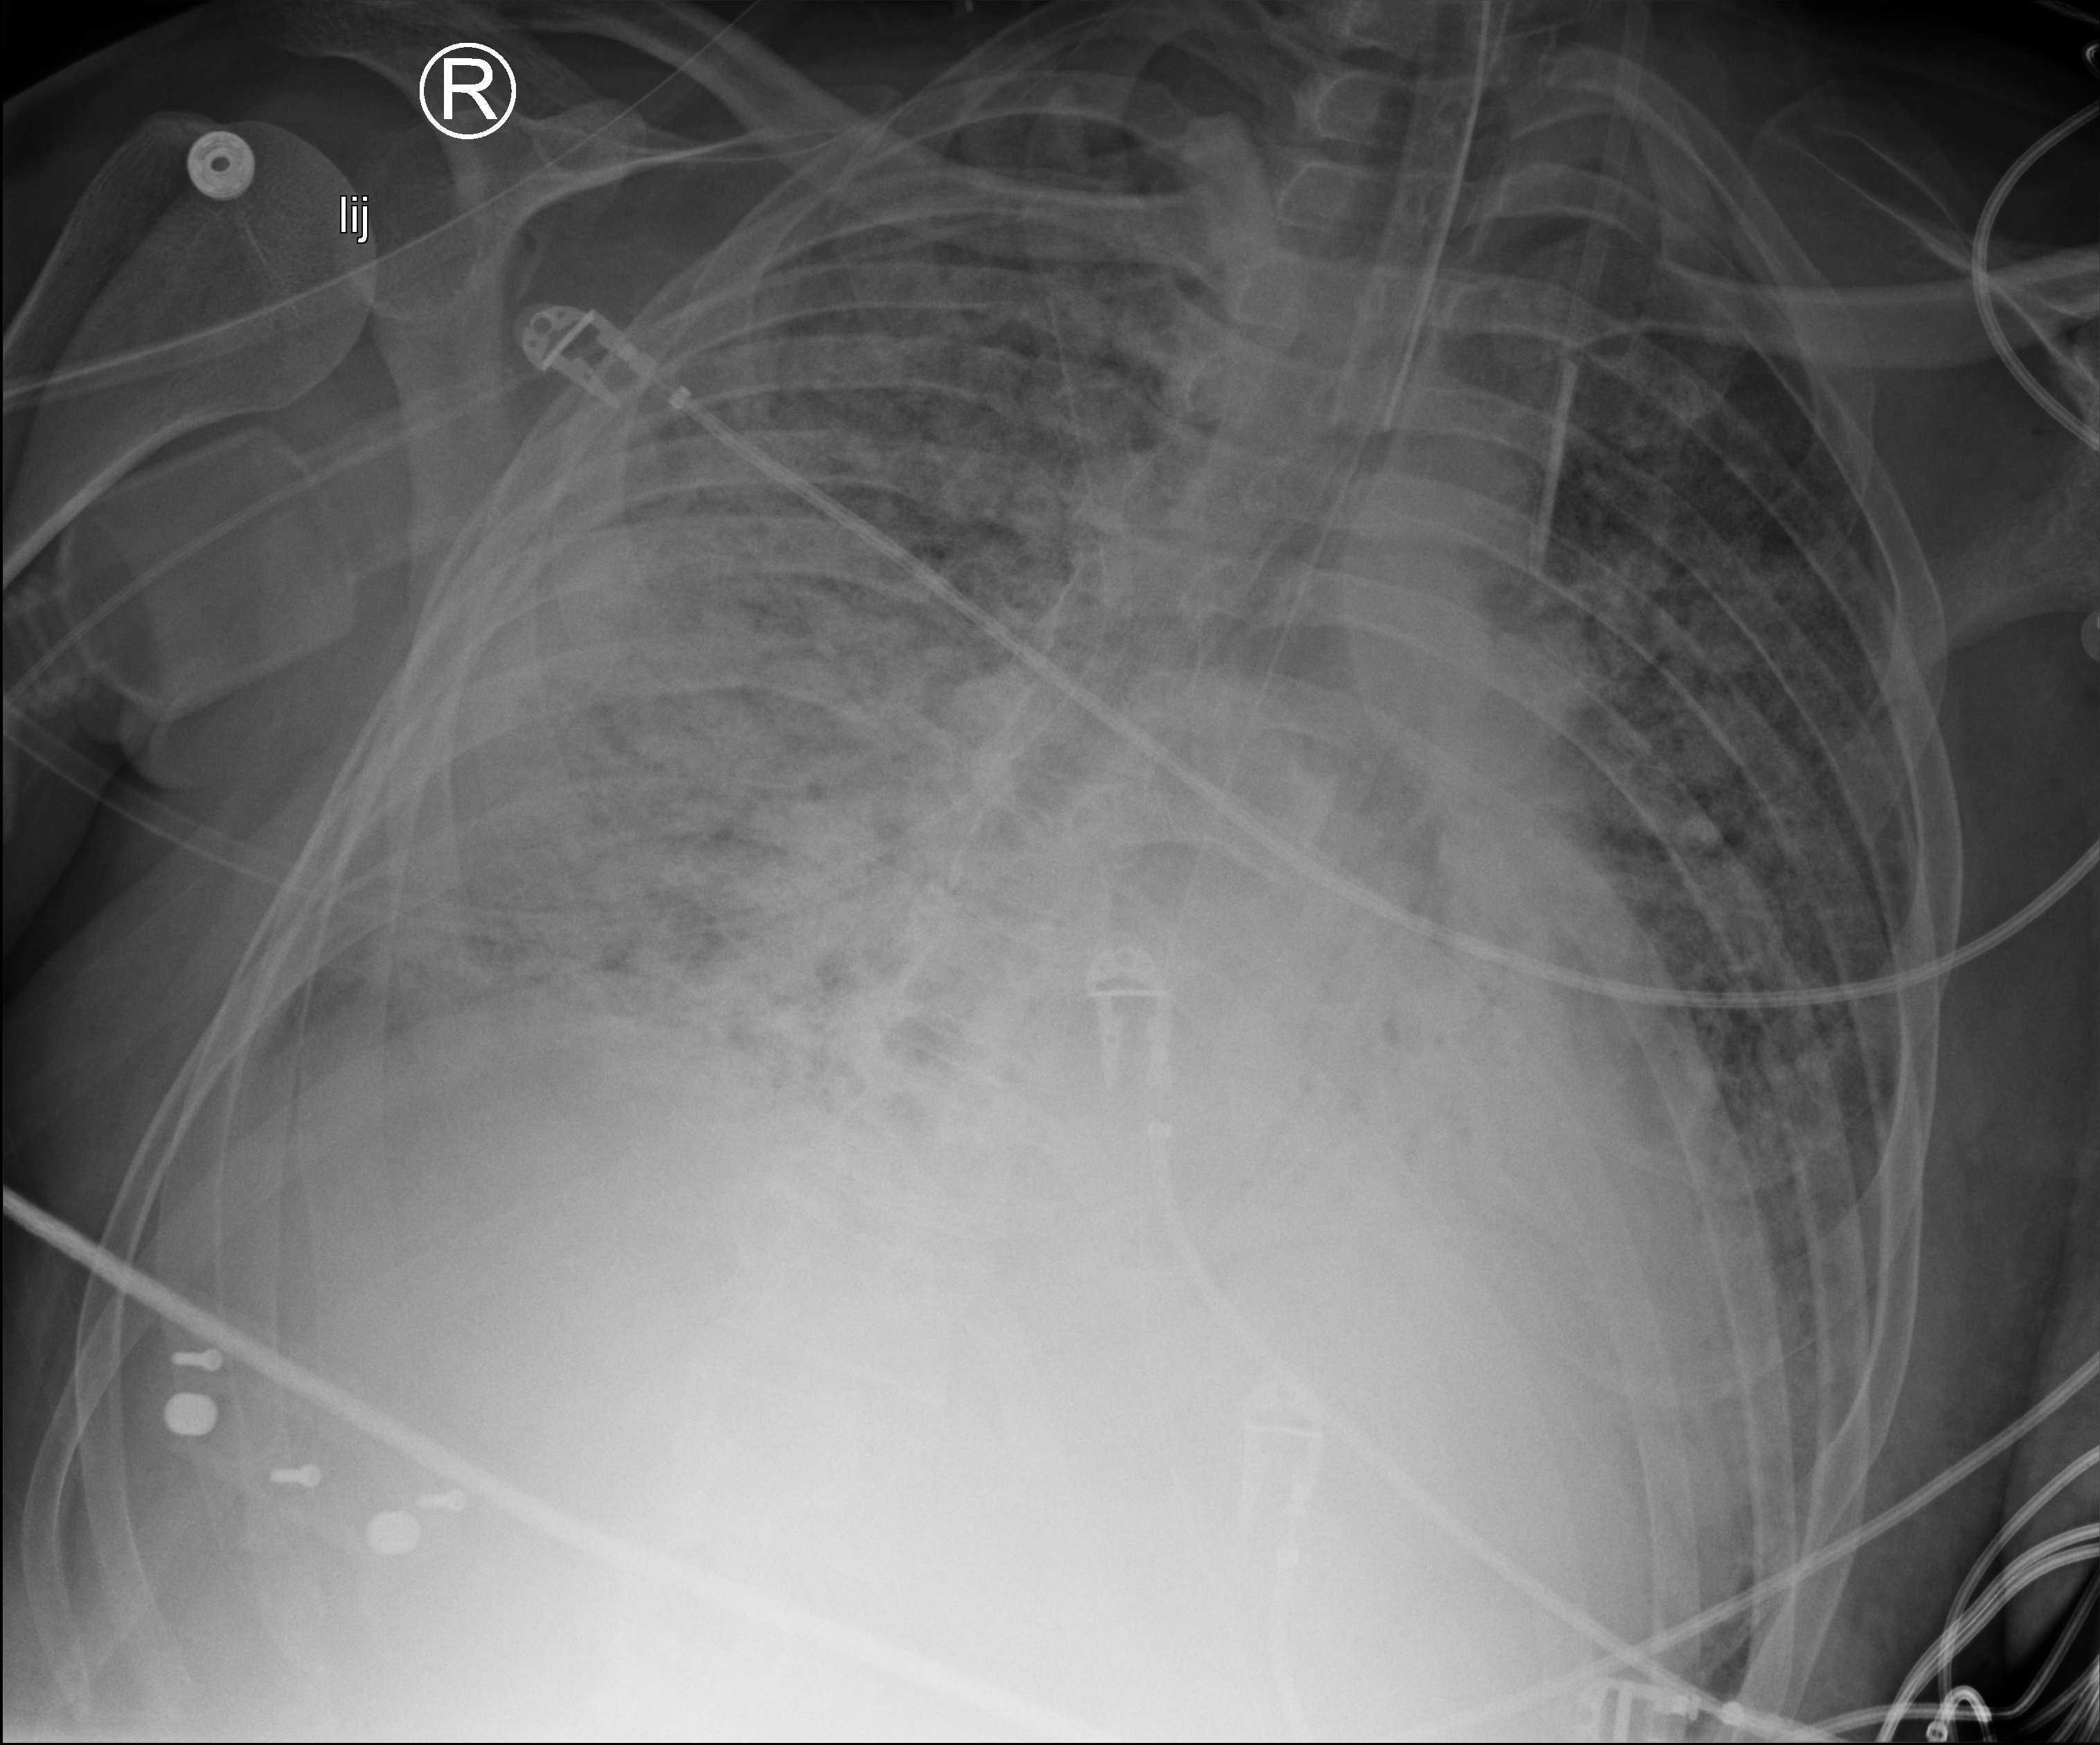
Bedside chest radiograph (computed radiography), anteroposterior (AP) projection. Patient hospitalised with COVID-19; male, aged 18–59 years.
Hospital-stay facts (about this admission, not read from this image; timing relative to this image not recorded):
- smoking status (admission record): never
- other chronic lung disease (admission record): no